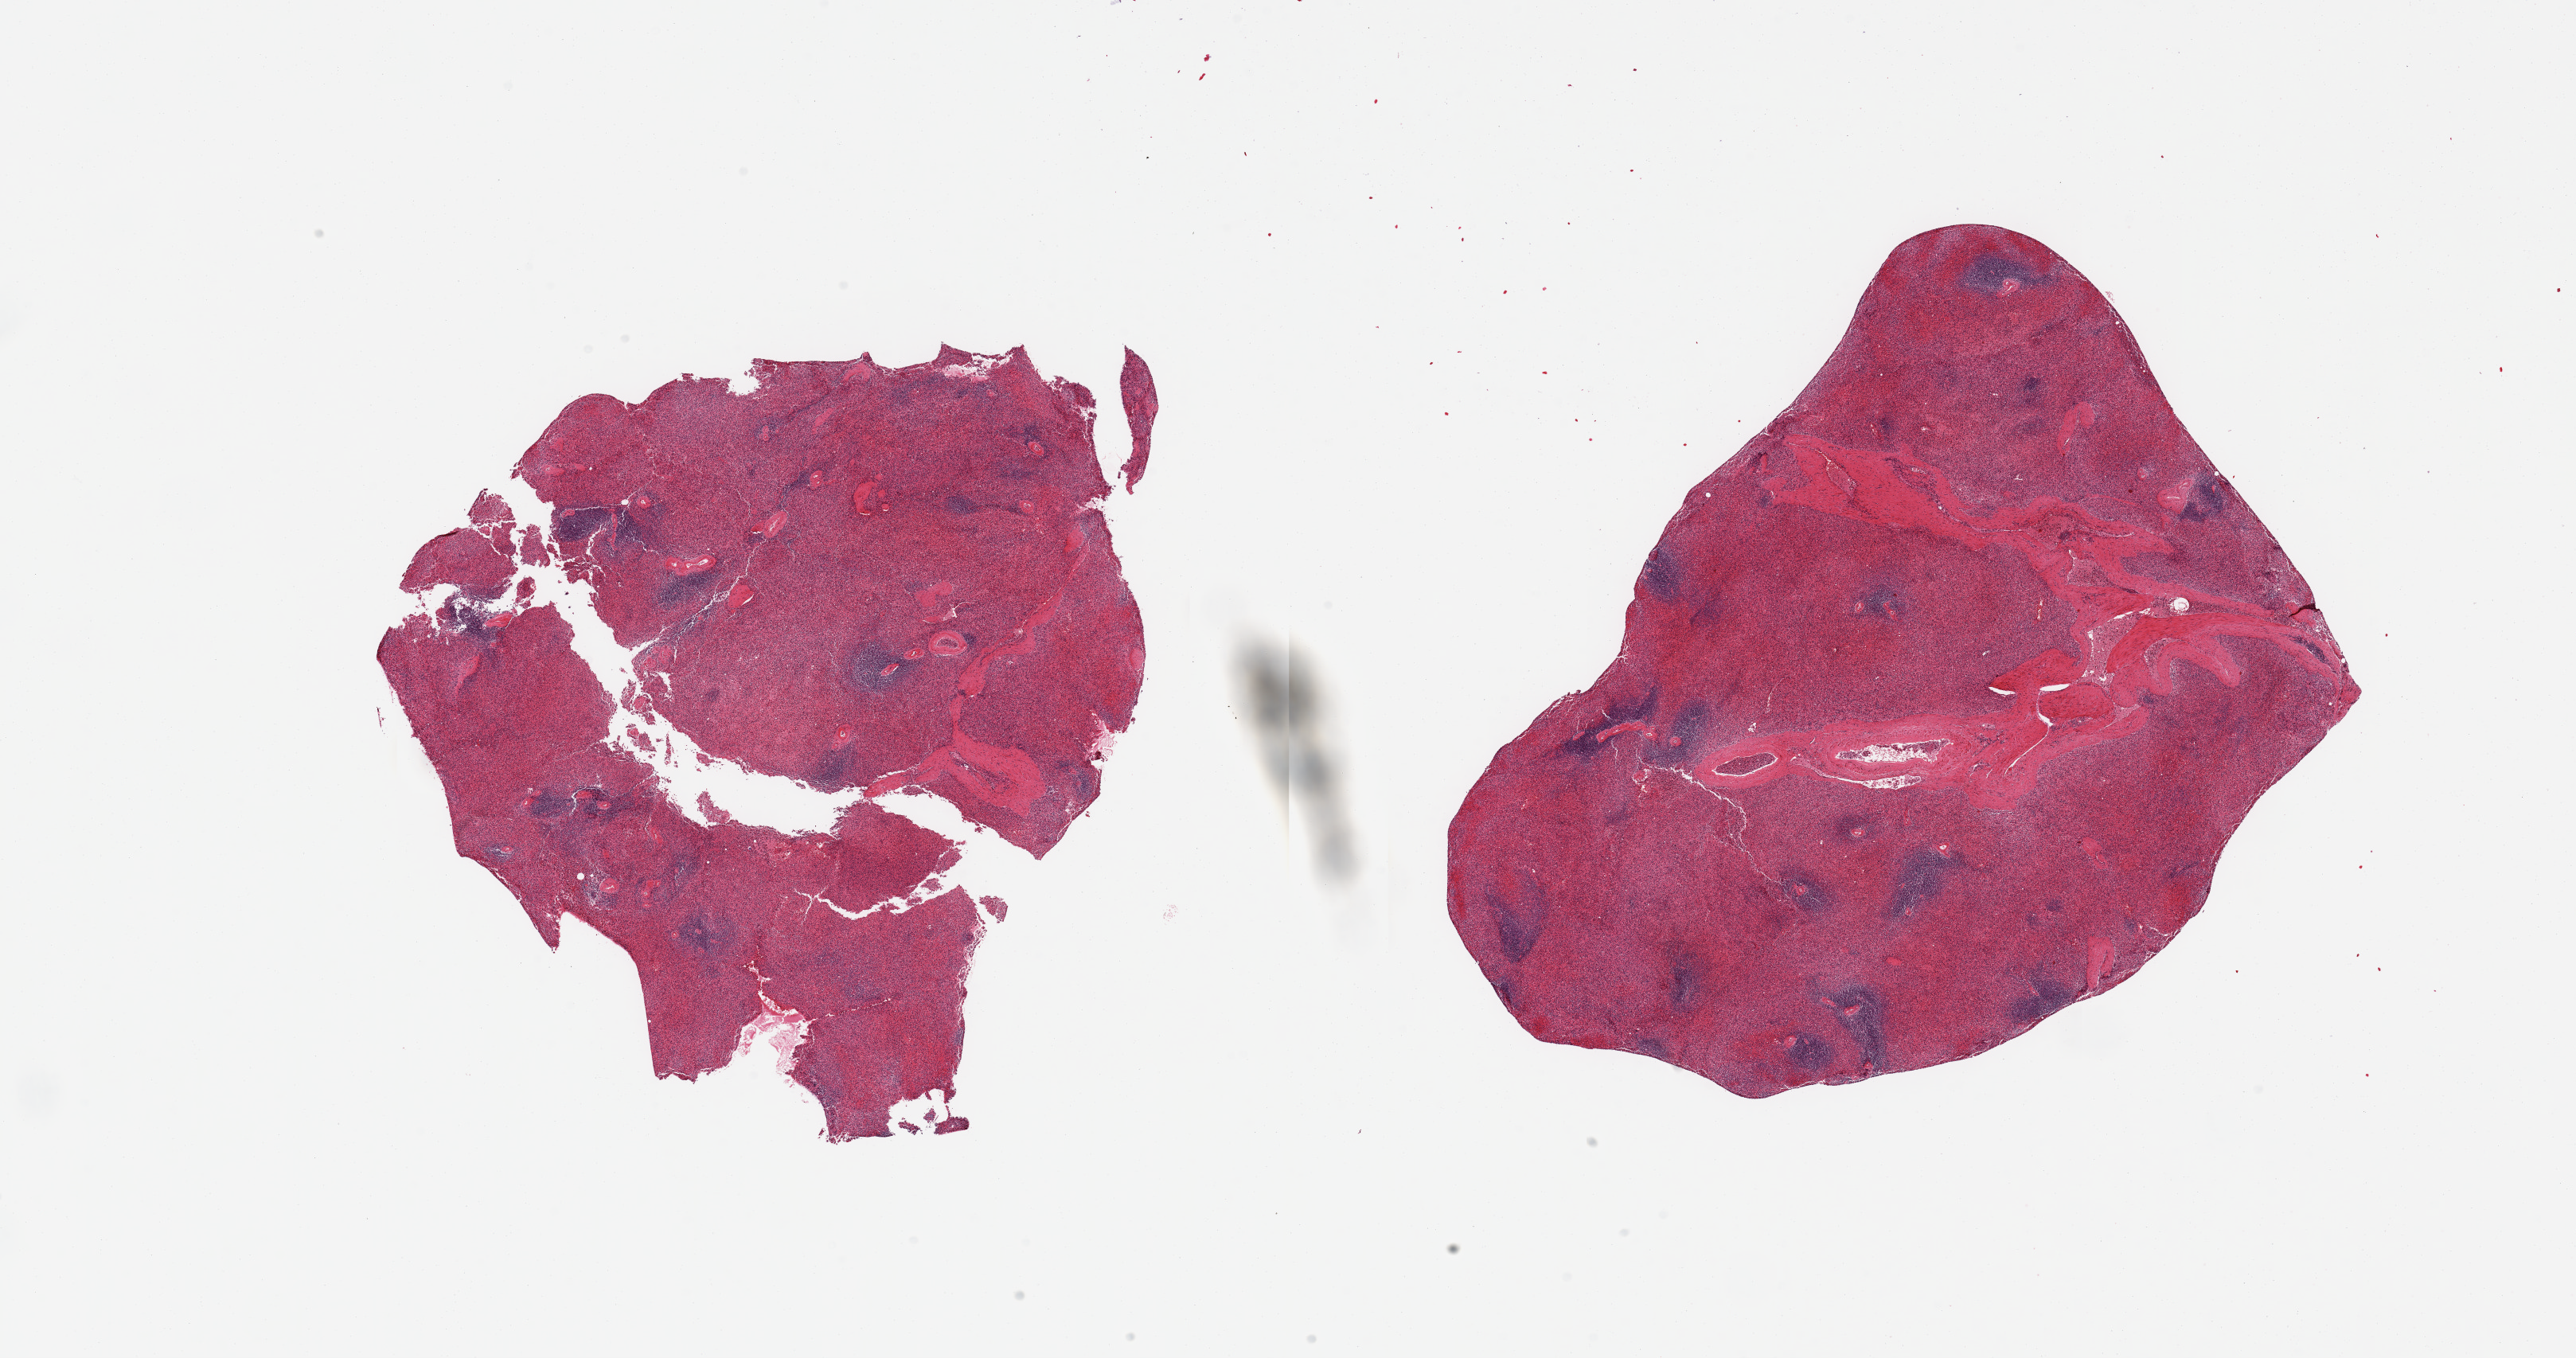
Digitized H&E-stained section, low-resolution overview of the scanned area, about 25.6 x 13.5 mm (slide scanned at 20x). PAXgene-fixed paraffin-embedded (PFPE) section. Section of spleen (target tissue). Donor tissue sample. Donor sex: male.
Review note (as recorded): 2 pieces; well preserved lymphoid tissue.